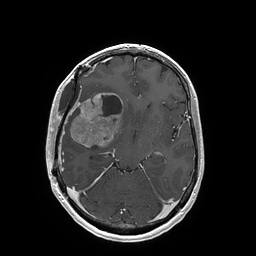
Brain MRI from a brain-tumour surgery series, one axial slice; slice 99 of 202 in the series (ordered by position); T1-weighted post-contrast; 1 mm slice thickness; 256 × 256 image matrix, field of view 250 × 250 mm. Case-level facts recorded for this patient, not image findings: histopathology: Glioblastoma; WHO grade: 4; IDH mutation: no; tumour location: Right Insular.
Outlined on this slice (outlined manually by an expert reader):
- tumour: box from (x=69, y=93) to (x=122, y=148) px